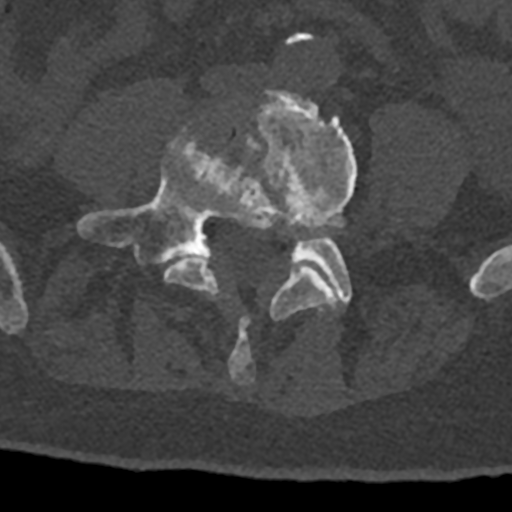
CT including the spine, one axial slice; position 227 of 797 along the scan axis; reconstruction kernel Br40s/3; 120 kVp; bone window (W 1800 / L 400 HU); 0.5 mm slice thickness; 512 × 512 image matrix, field of view 160 × 160 mm. Patient: male, 74 years. From the clinical record (not read from this slice): primary cancer: renal.
Outlined on this slice (semi-automatic segmentation, software-assisted and operator-edited):
- L4 vertebra: box from (x=163, y=90) to (x=357, y=384) px
- L5 vertebra: (x=77, y=130)–(x=352, y=304)